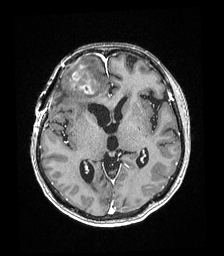
Brain MRI from a brain-tumour surgery series, one axial slice. Slice 102 of 192 in the series (ordered by position). T1-weighted post-contrast. 1 mm slice thickness. 224 × 256 image matrix, field of view 219 × 250 mm. Case-level facts recorded for this patient, not image findings: histopathology: Astrocytoma; WHO grade: 4; IDH mutation: yes; tumour location: Right superficial frontal.
Outlined on this slice (outlined manually by an expert reader):
- tumour: bounding box (x1, y1, x2, y2) in pixels: (72, 66, 96, 94)